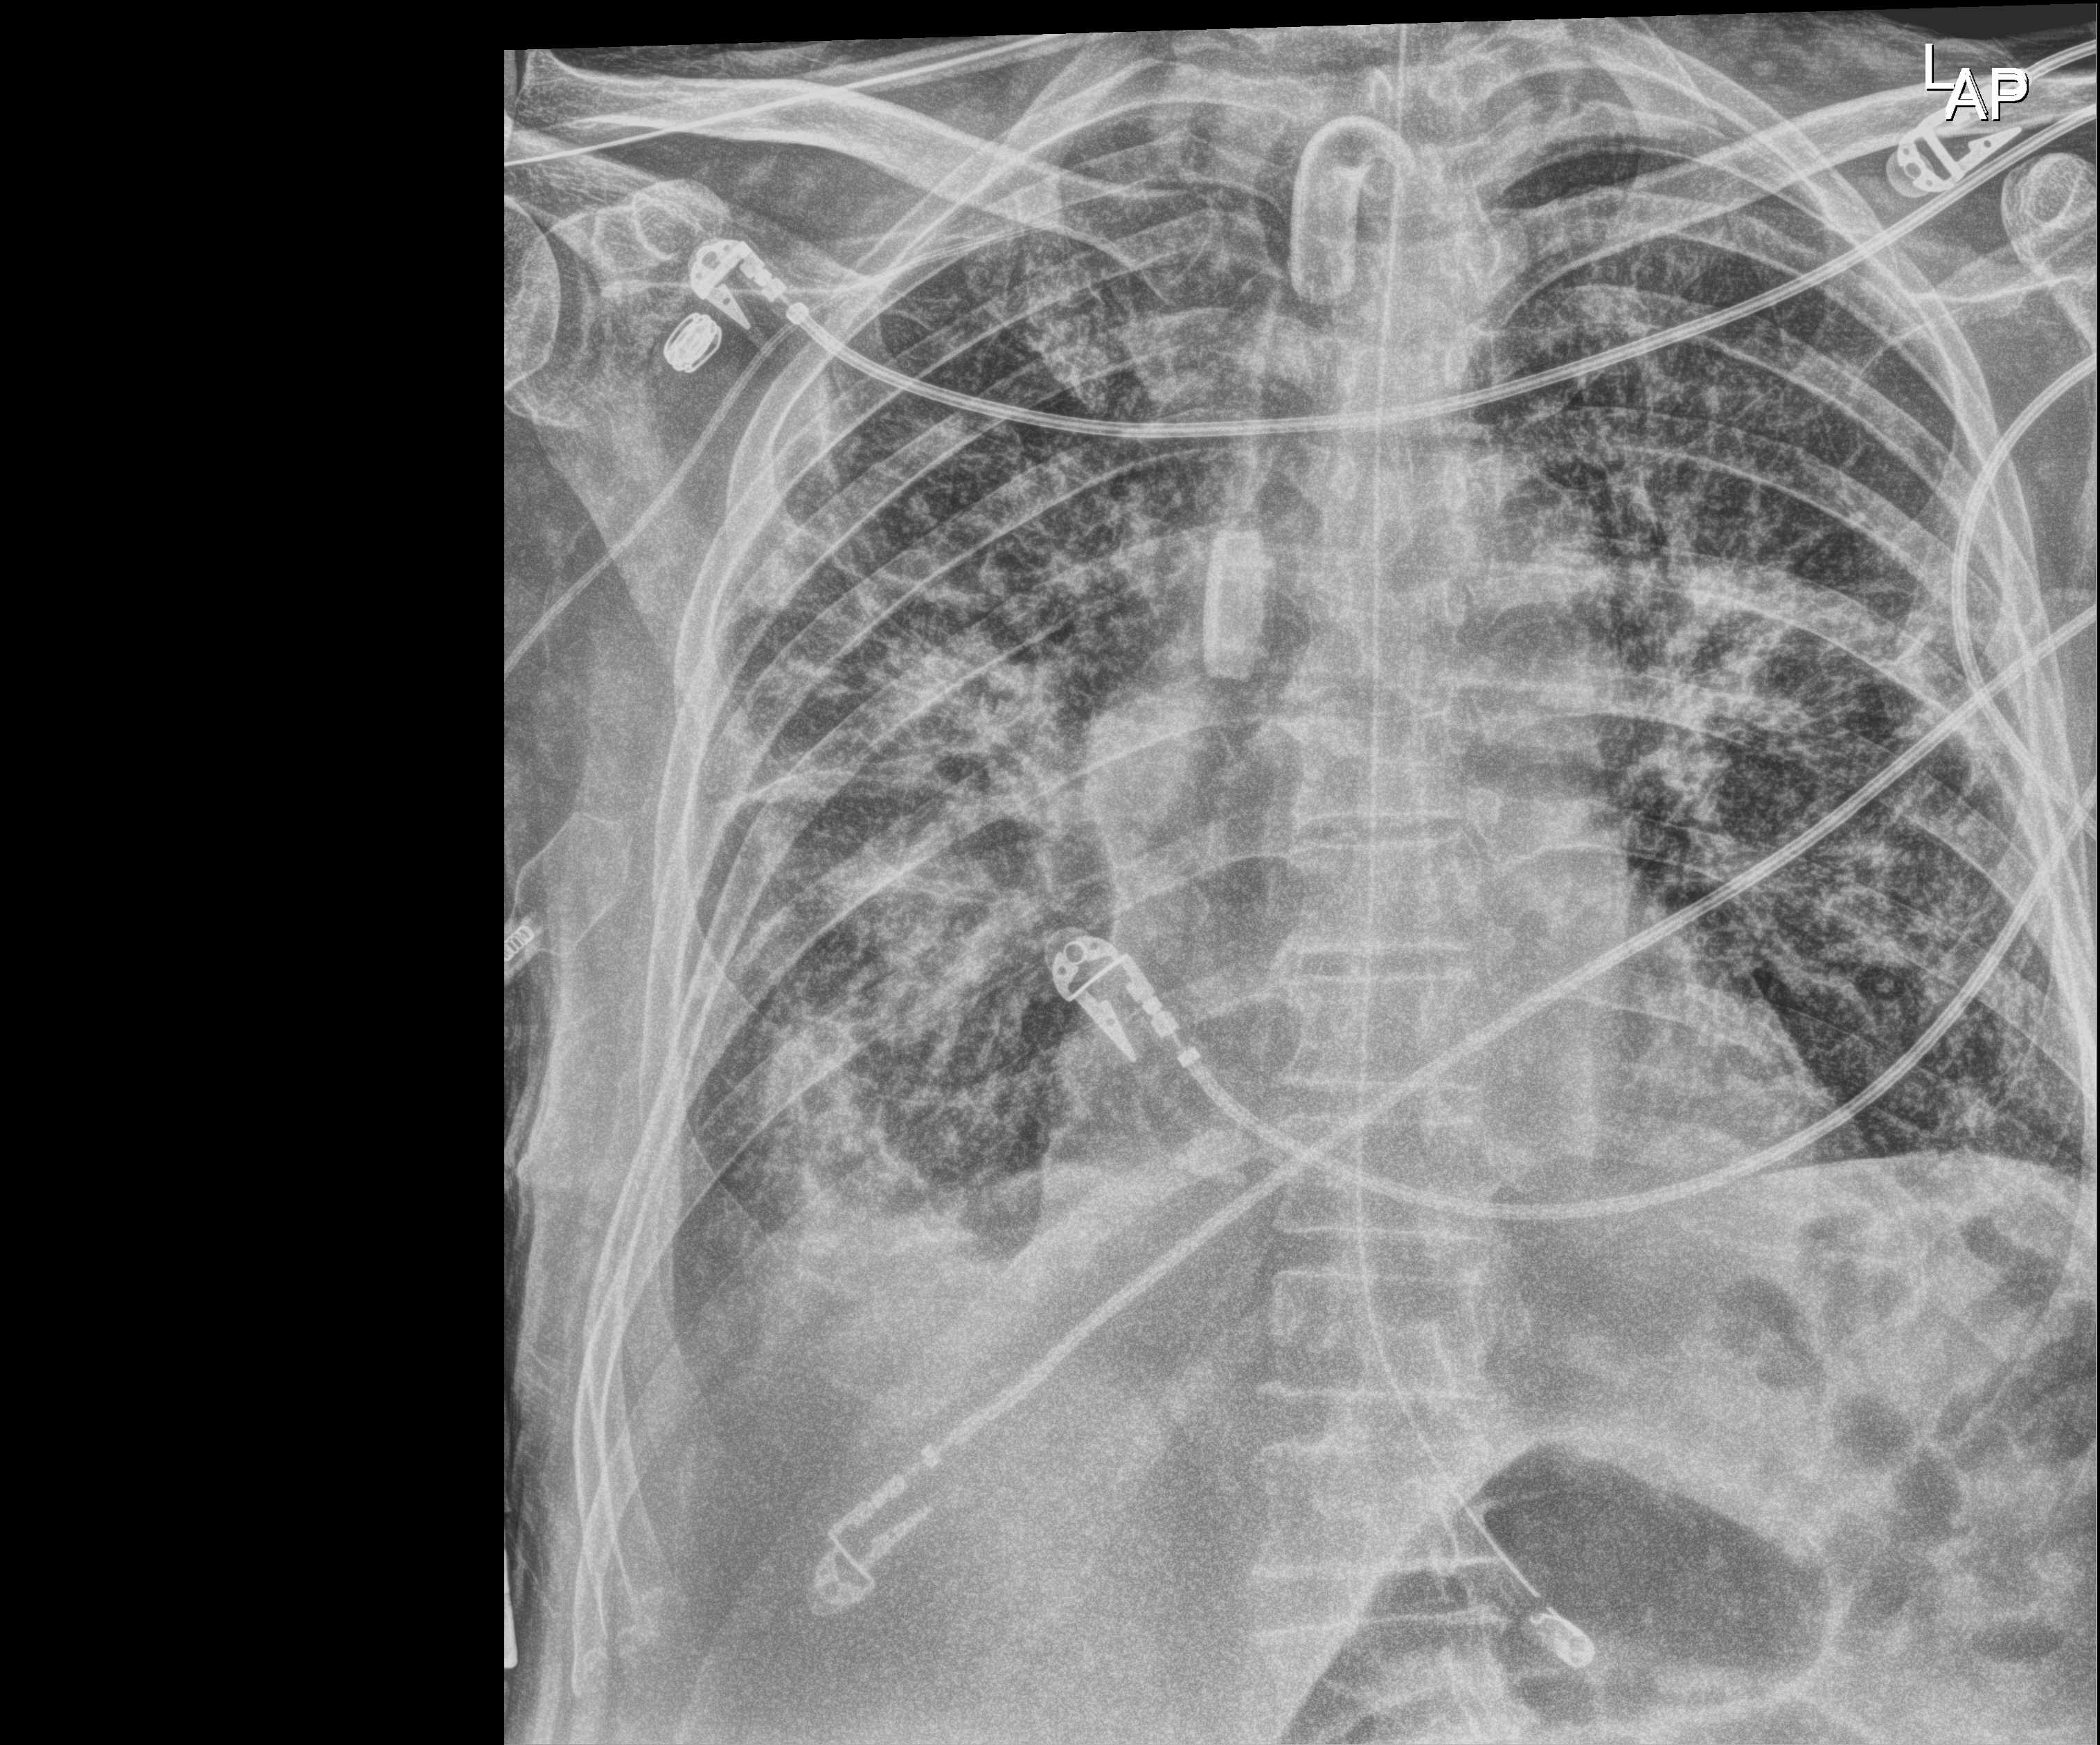
Portable chest radiograph. Patient hospitalised with COVID-19; male, aged 75–90 years.
Hospital-stay facts (about this admission, not read from this image; timing relative to this image not recorded): length of hospital stay: 70 days; mechanically ventilated during this hospital stay: yes.